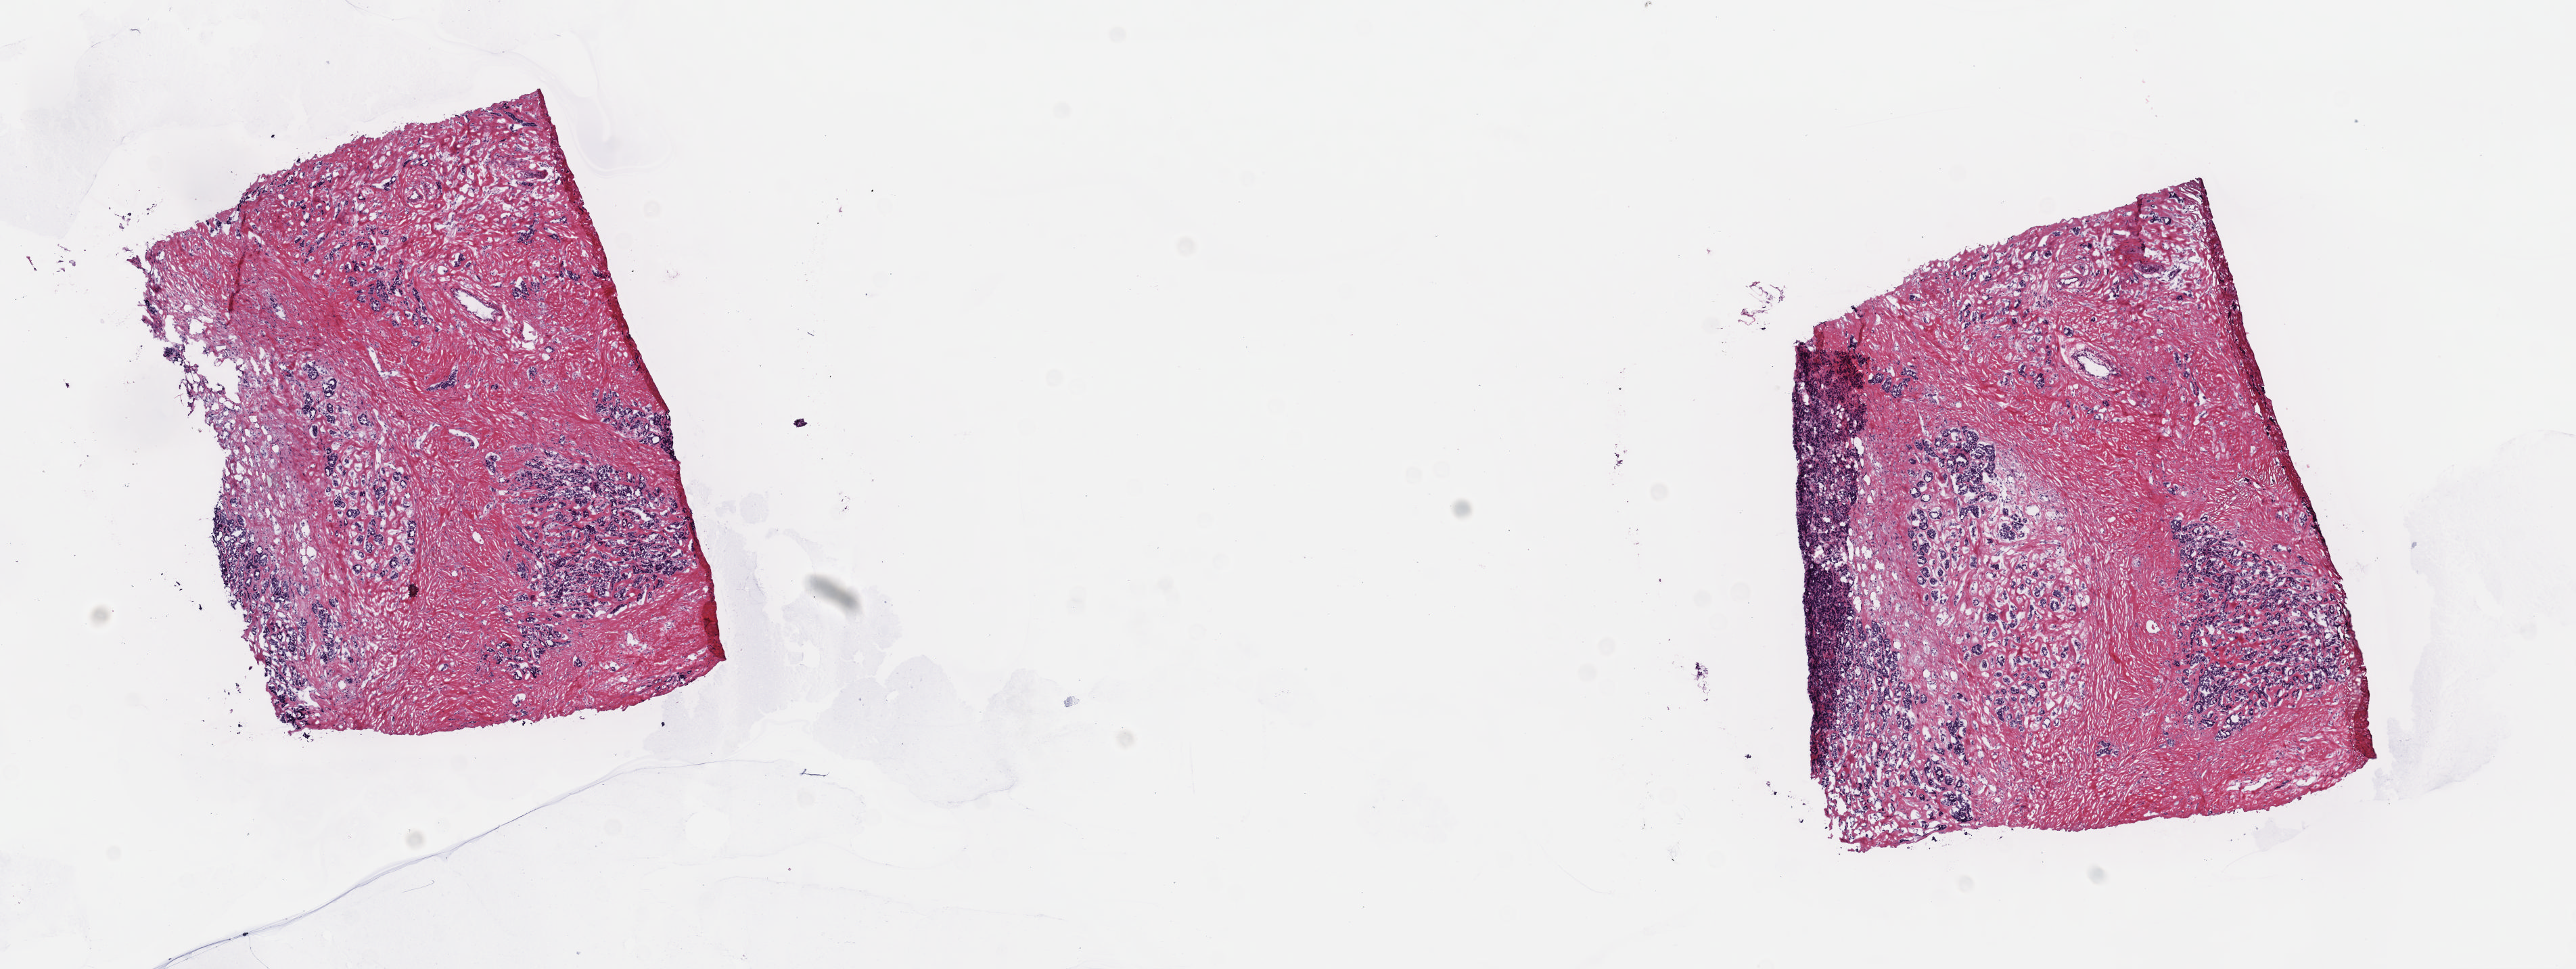
Whole-slide histology image, H&E-stained, a low-resolution overview of the entire scanned area, about 15.0 x 5.6 mm (slide scanned at 40x); frozen section; breast, primary tumour sample. Female patient; age at initial diagnosis 56 years. Slide review estimates, as recorded: tumour cells 50%, tumour nuclei 70%, normal cells 0%, stromal cells 50%, necrosis 0%. Inflammatory infiltration, as recorded: lymphocyte infiltration 0%, monocyte infiltration 0%, neutrophil infiltration 0%.
Laterality: right. Lymph nodes positive (case pathology): 2 of 7 examined. AJCC pathologic stage: IIB (7th edition). Diagnosis: Infiltrating duct carcinoma, NOS.